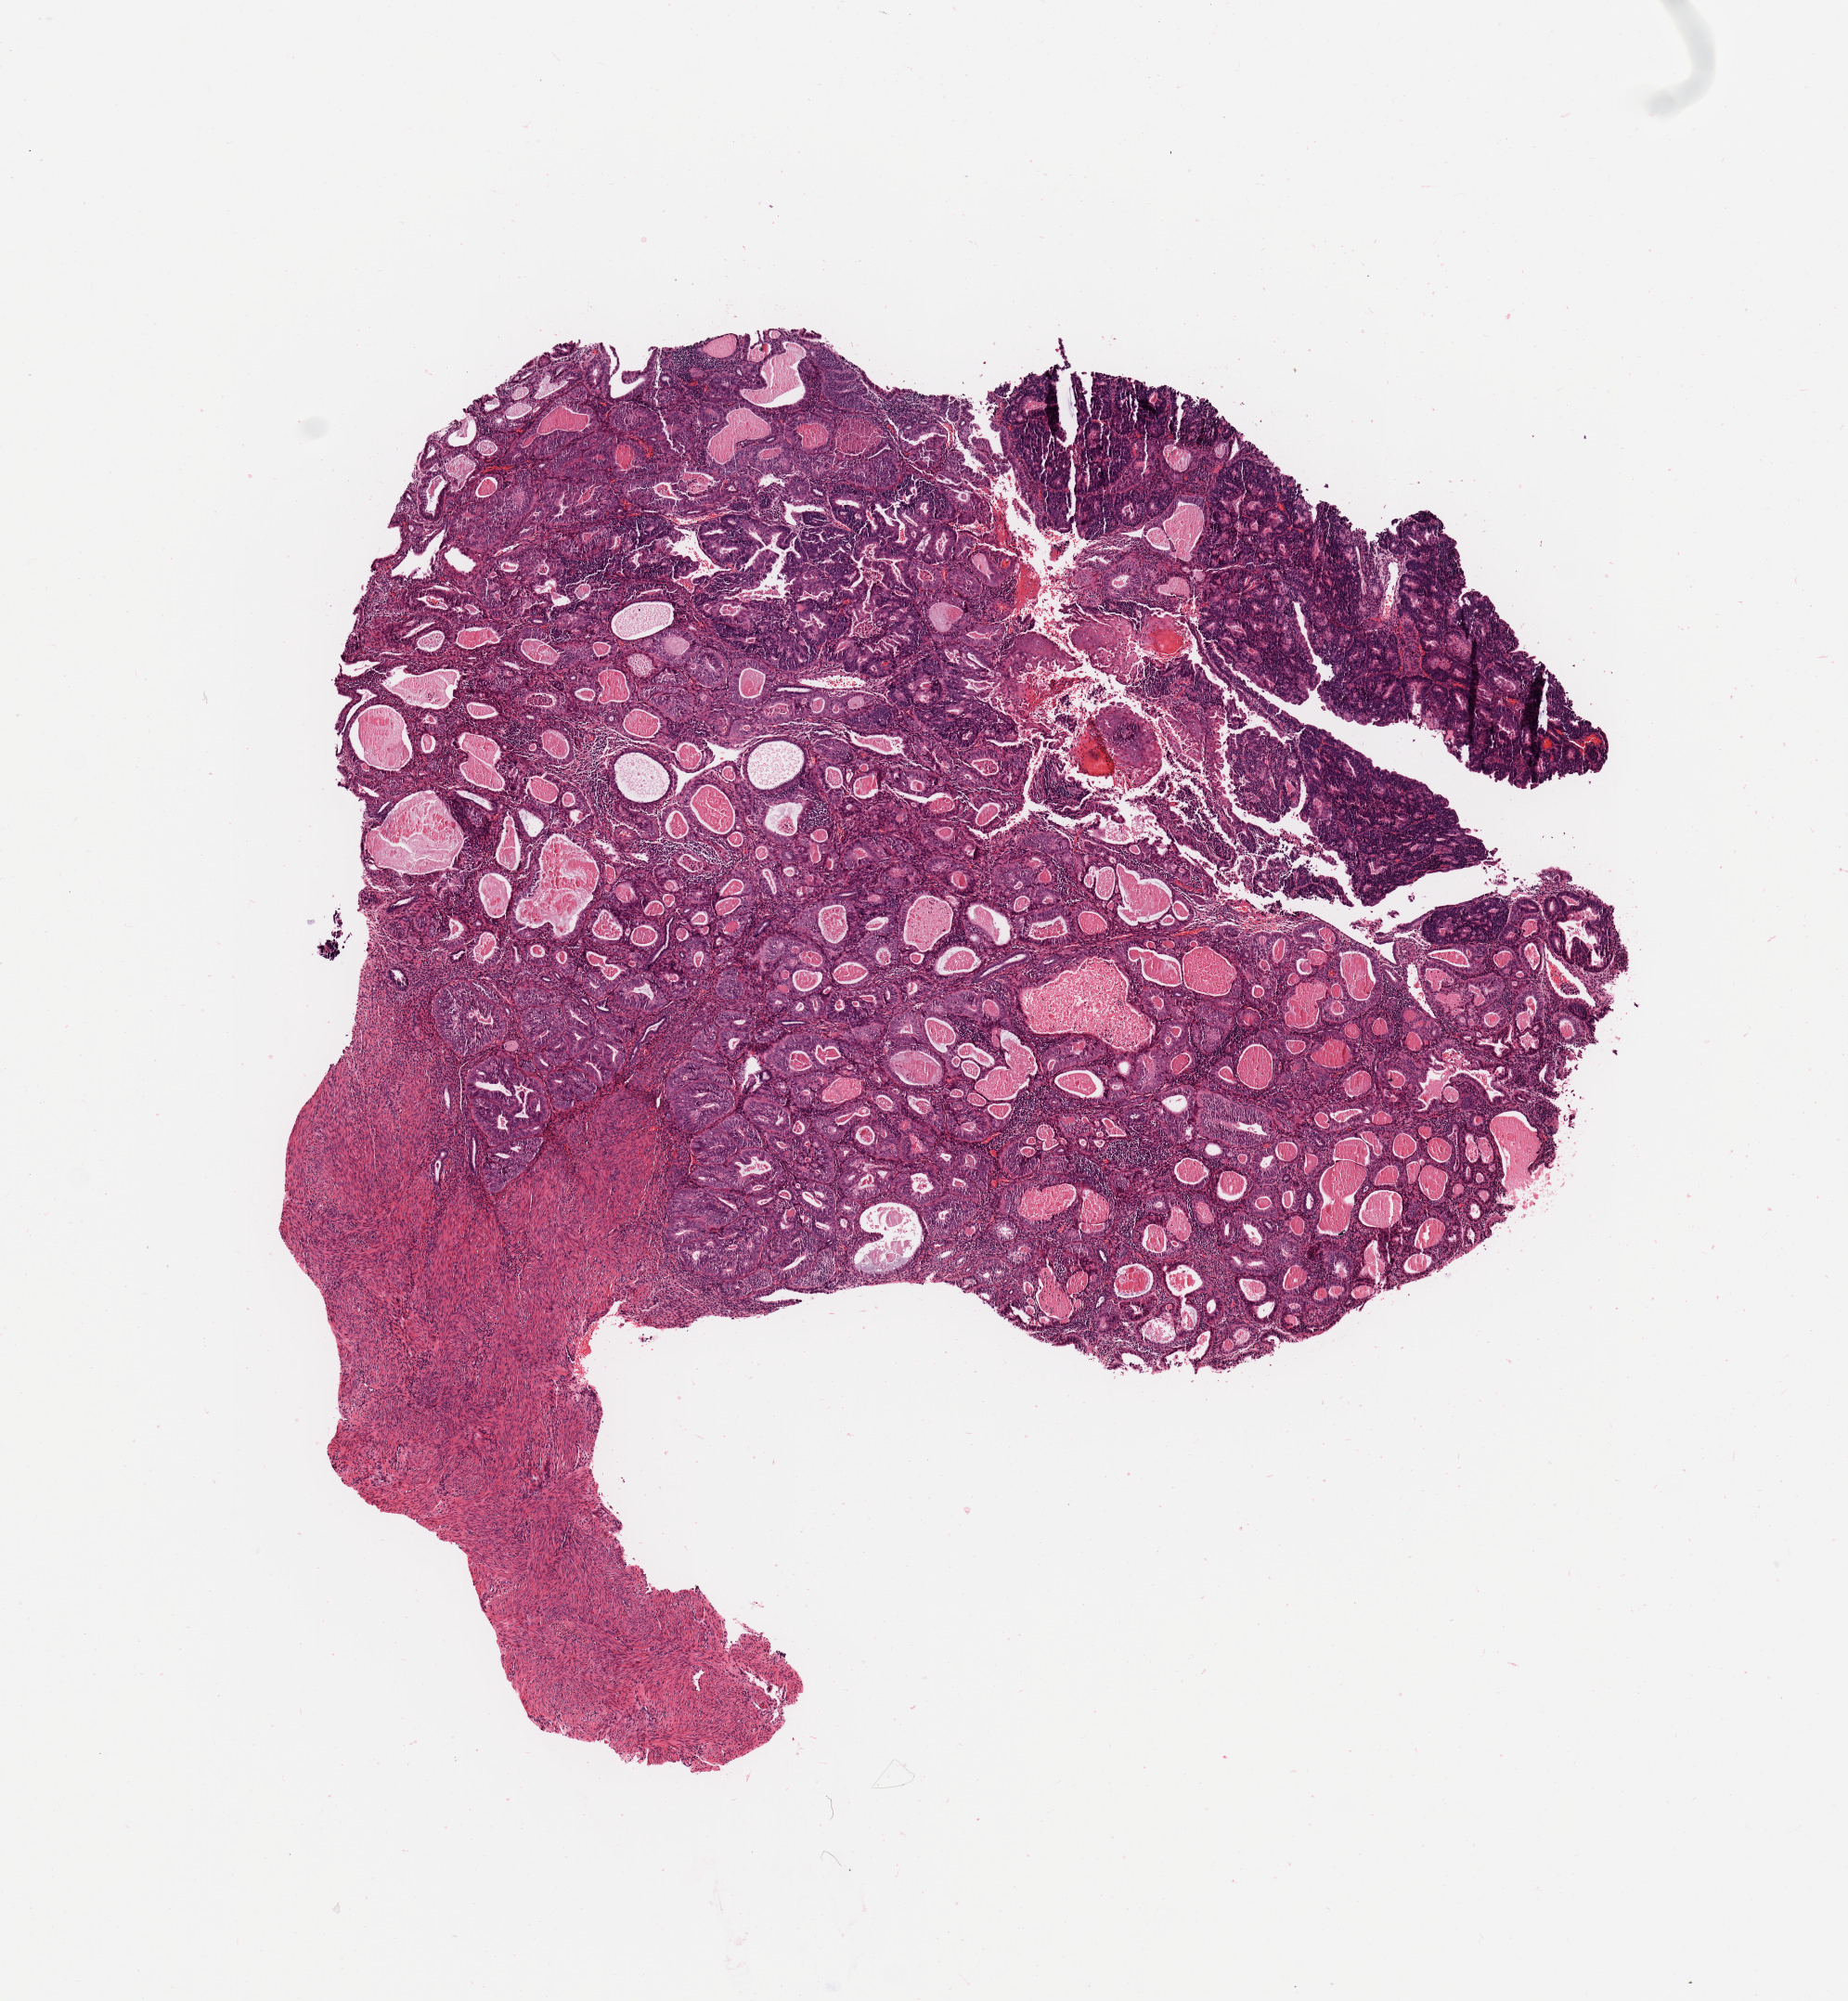
Digitized H&E tissue section (whole slide), whole scanned area (about 7.9 x 8.5 mm) shown as a low-resolution overview; tumour tissue sample, uterus. 66-year-old female patient. Histologic grade: G2 (moderately differentiated).
Histologic diagnosis: Endometrioid adenocarcinoma, NOS. AJCC pathologic stage: IA.